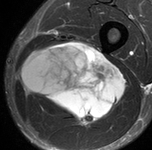
MRI of an extremity soft-tissue mass, one axial slice. Position 50 of 90 along the scan axis. STIR. MR volume resampled by the dataset authors to the PET/CT grid (not the native acquisition matrix). 3.27 mm slice thickness. 152 × 150 image matrix. Male patient. Case-level facts recorded for this patient, not image findings: histological type: undifferentiated pleomorphic liposarcoma; grade: high; site of the primary tumour: left thigh.
Outlined on this slice (expert contour drawn on MRI and transferred to this co-registered scan by the dataset authors):
- gross tumour volume including surrounding oedema: bounding box <20,43,128,127> (left, top, right, bottom; pixels)
- gross tumour volume (mass): <20,43,128,127>